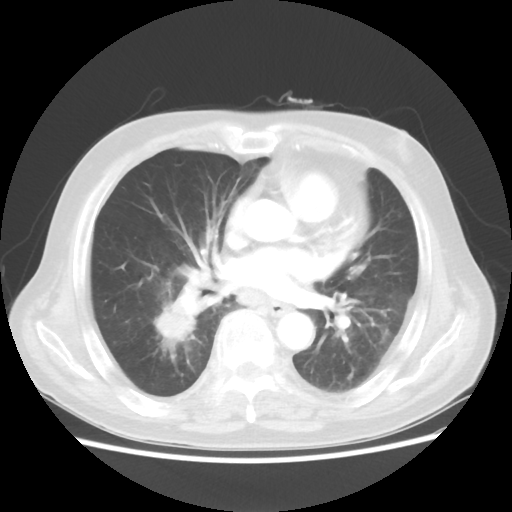
Chest CT, one axial slice. Slice 18 of 44 in the series (ordered by position). 100 kVp. Lung window (W 1500 / L -600 HU). 5 mm slice thickness. 512 × 512 image matrix. Male patient, age 83 years. Case-level facts recorded for this patient, not image findings: clinical TNM (as recorded): T2 N3 M0.
Outlined on this slice (bounding box drawn by a radiologist):
- lung tumour (recorded histology: adenocarcinoma): bounding box [x1, y1, x2, y2] px = [148, 289, 203, 350]